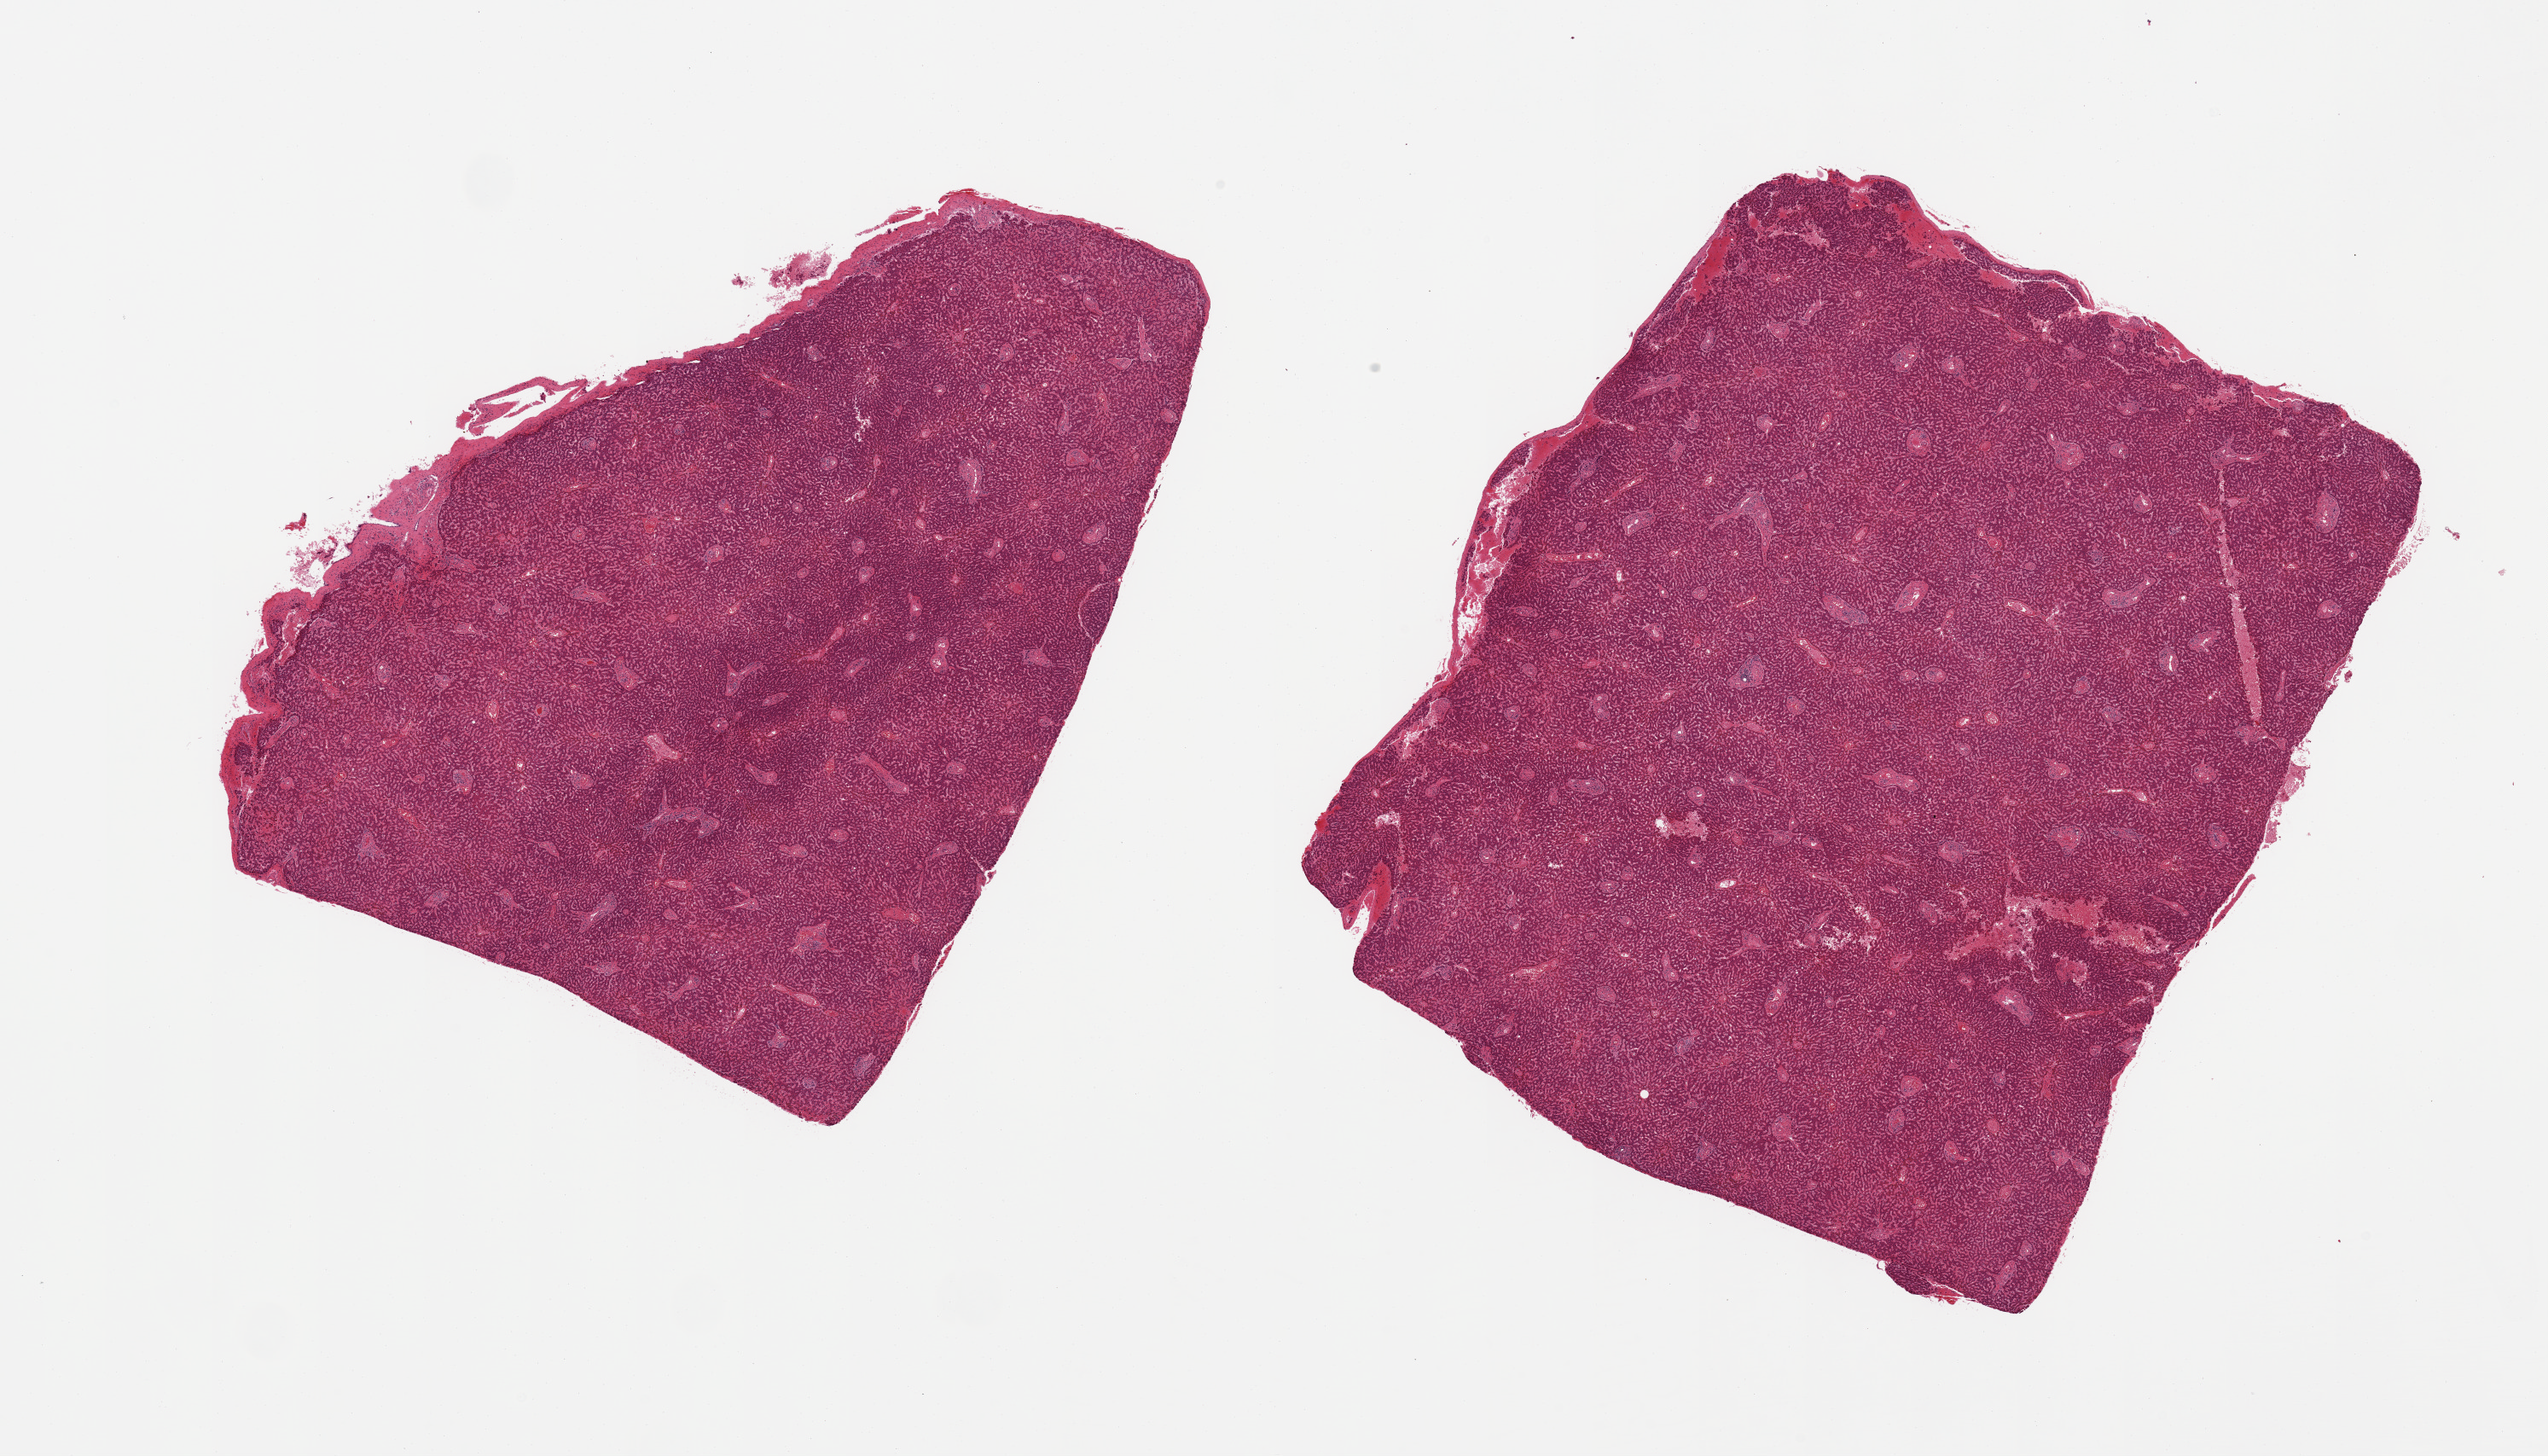
Haematoxylin and eosin whole-slide image, shown as a low-resolution overview of the whole scanned area (about 23.6 x 13.5 mm); PAXgene-fixed, paraffin-embedded tissue; sampled site (target tissue): liver; donor tissue sample. Male donor.
Pathologist's review note for this sample: 2 pieces; several focal hemorrhages; capsule sampled.